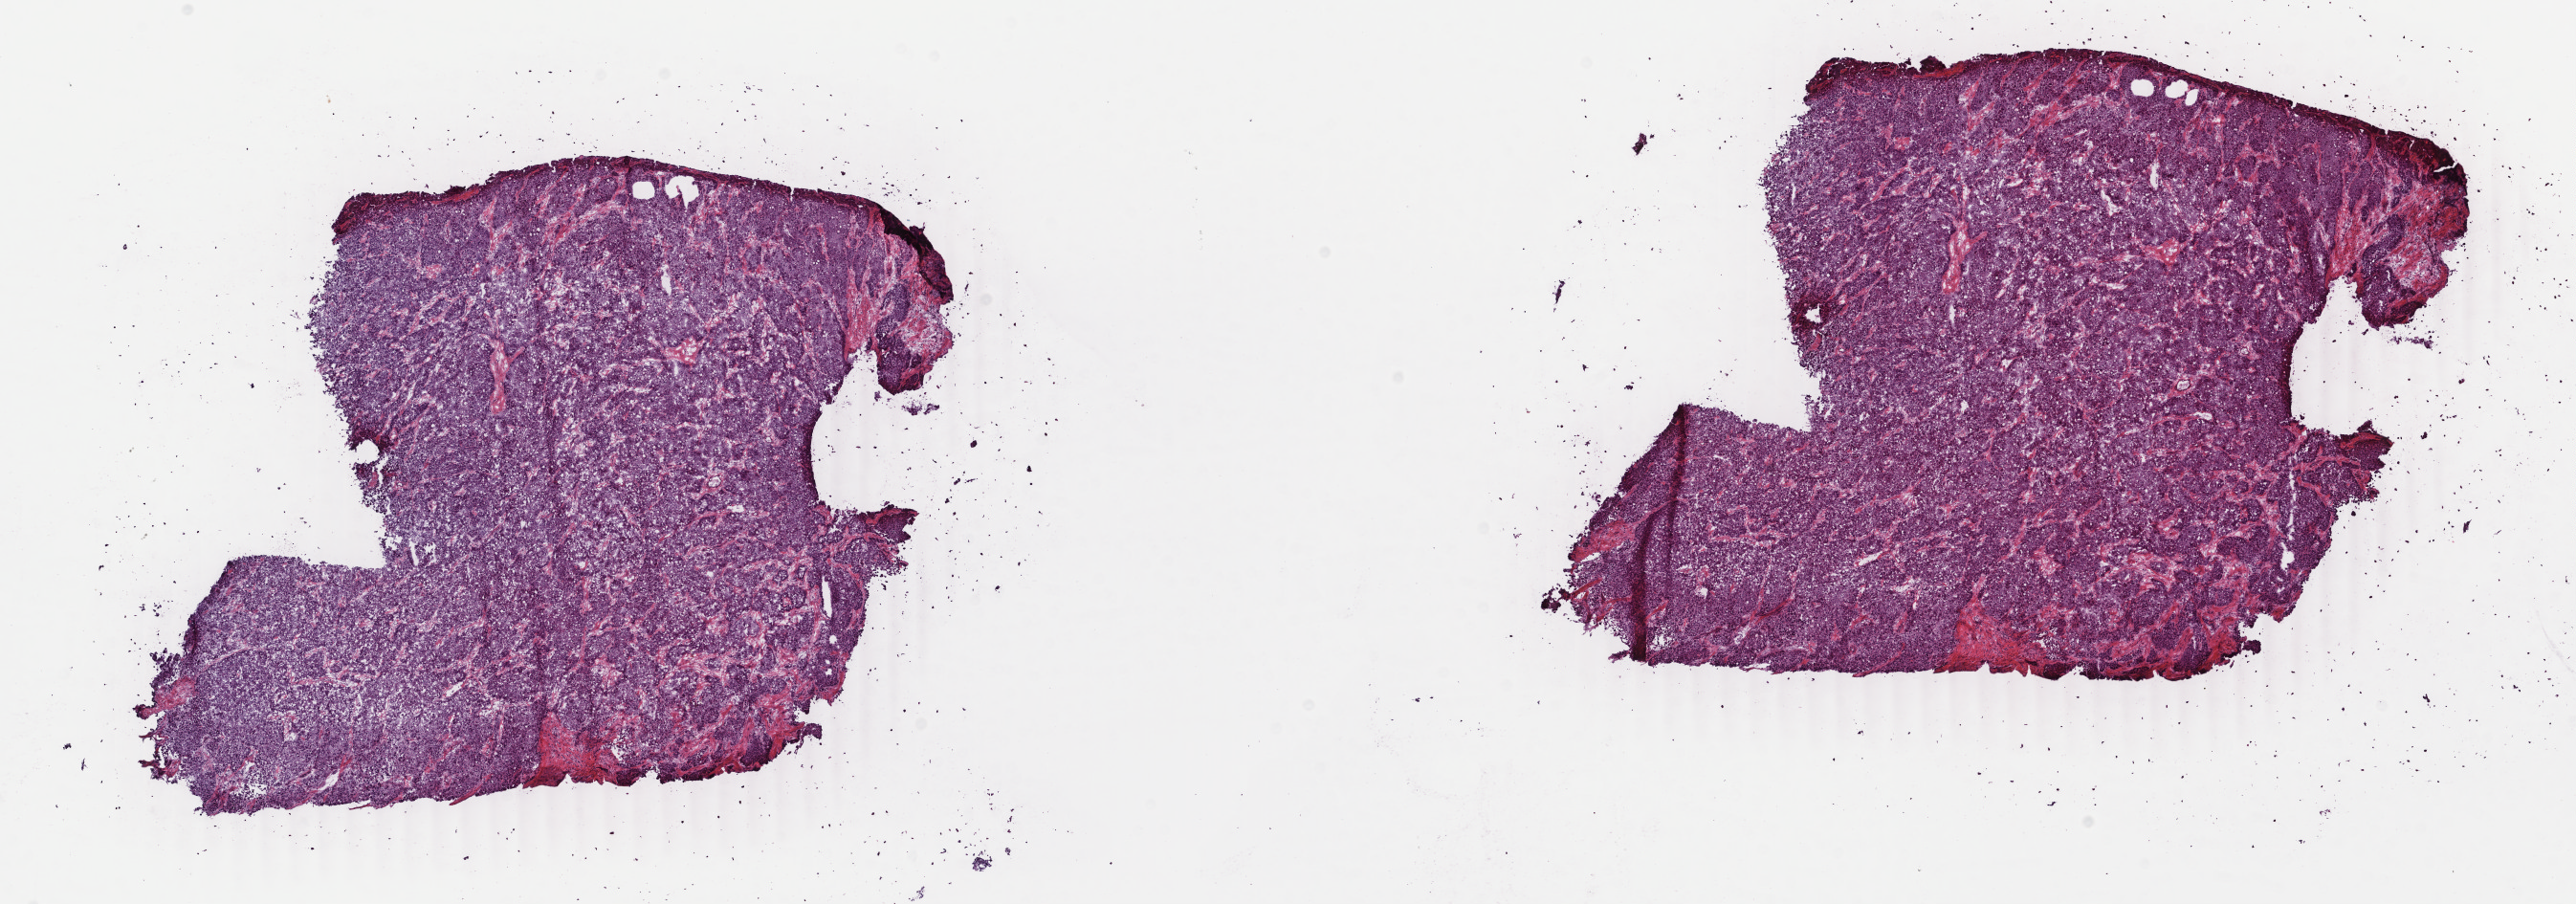
Hematoxylin and eosin (H&E) stained whole-slide image, shown as a low-resolution overview of the whole scanned area (about 21.4 x 7.5 mm); frozen section from the top of the tissue portion; sample: primary tumour, liver. Female, age 66 years at initial diagnosis. Histologic grade: G2 (moderately differentiated). Pathologist review of this section (percent, as recorded): tumour cells 100%, tumour nuclei 95%, normal cells 0%, stromal cells 0%, necrosis 0%. Infiltration values recorded for this section: lymphocyte infiltration 0%, monocyte infiltration 0%, neutrophil infiltration 0%.
Histologic diagnosis: Hepatocellular carcinoma, NOS.